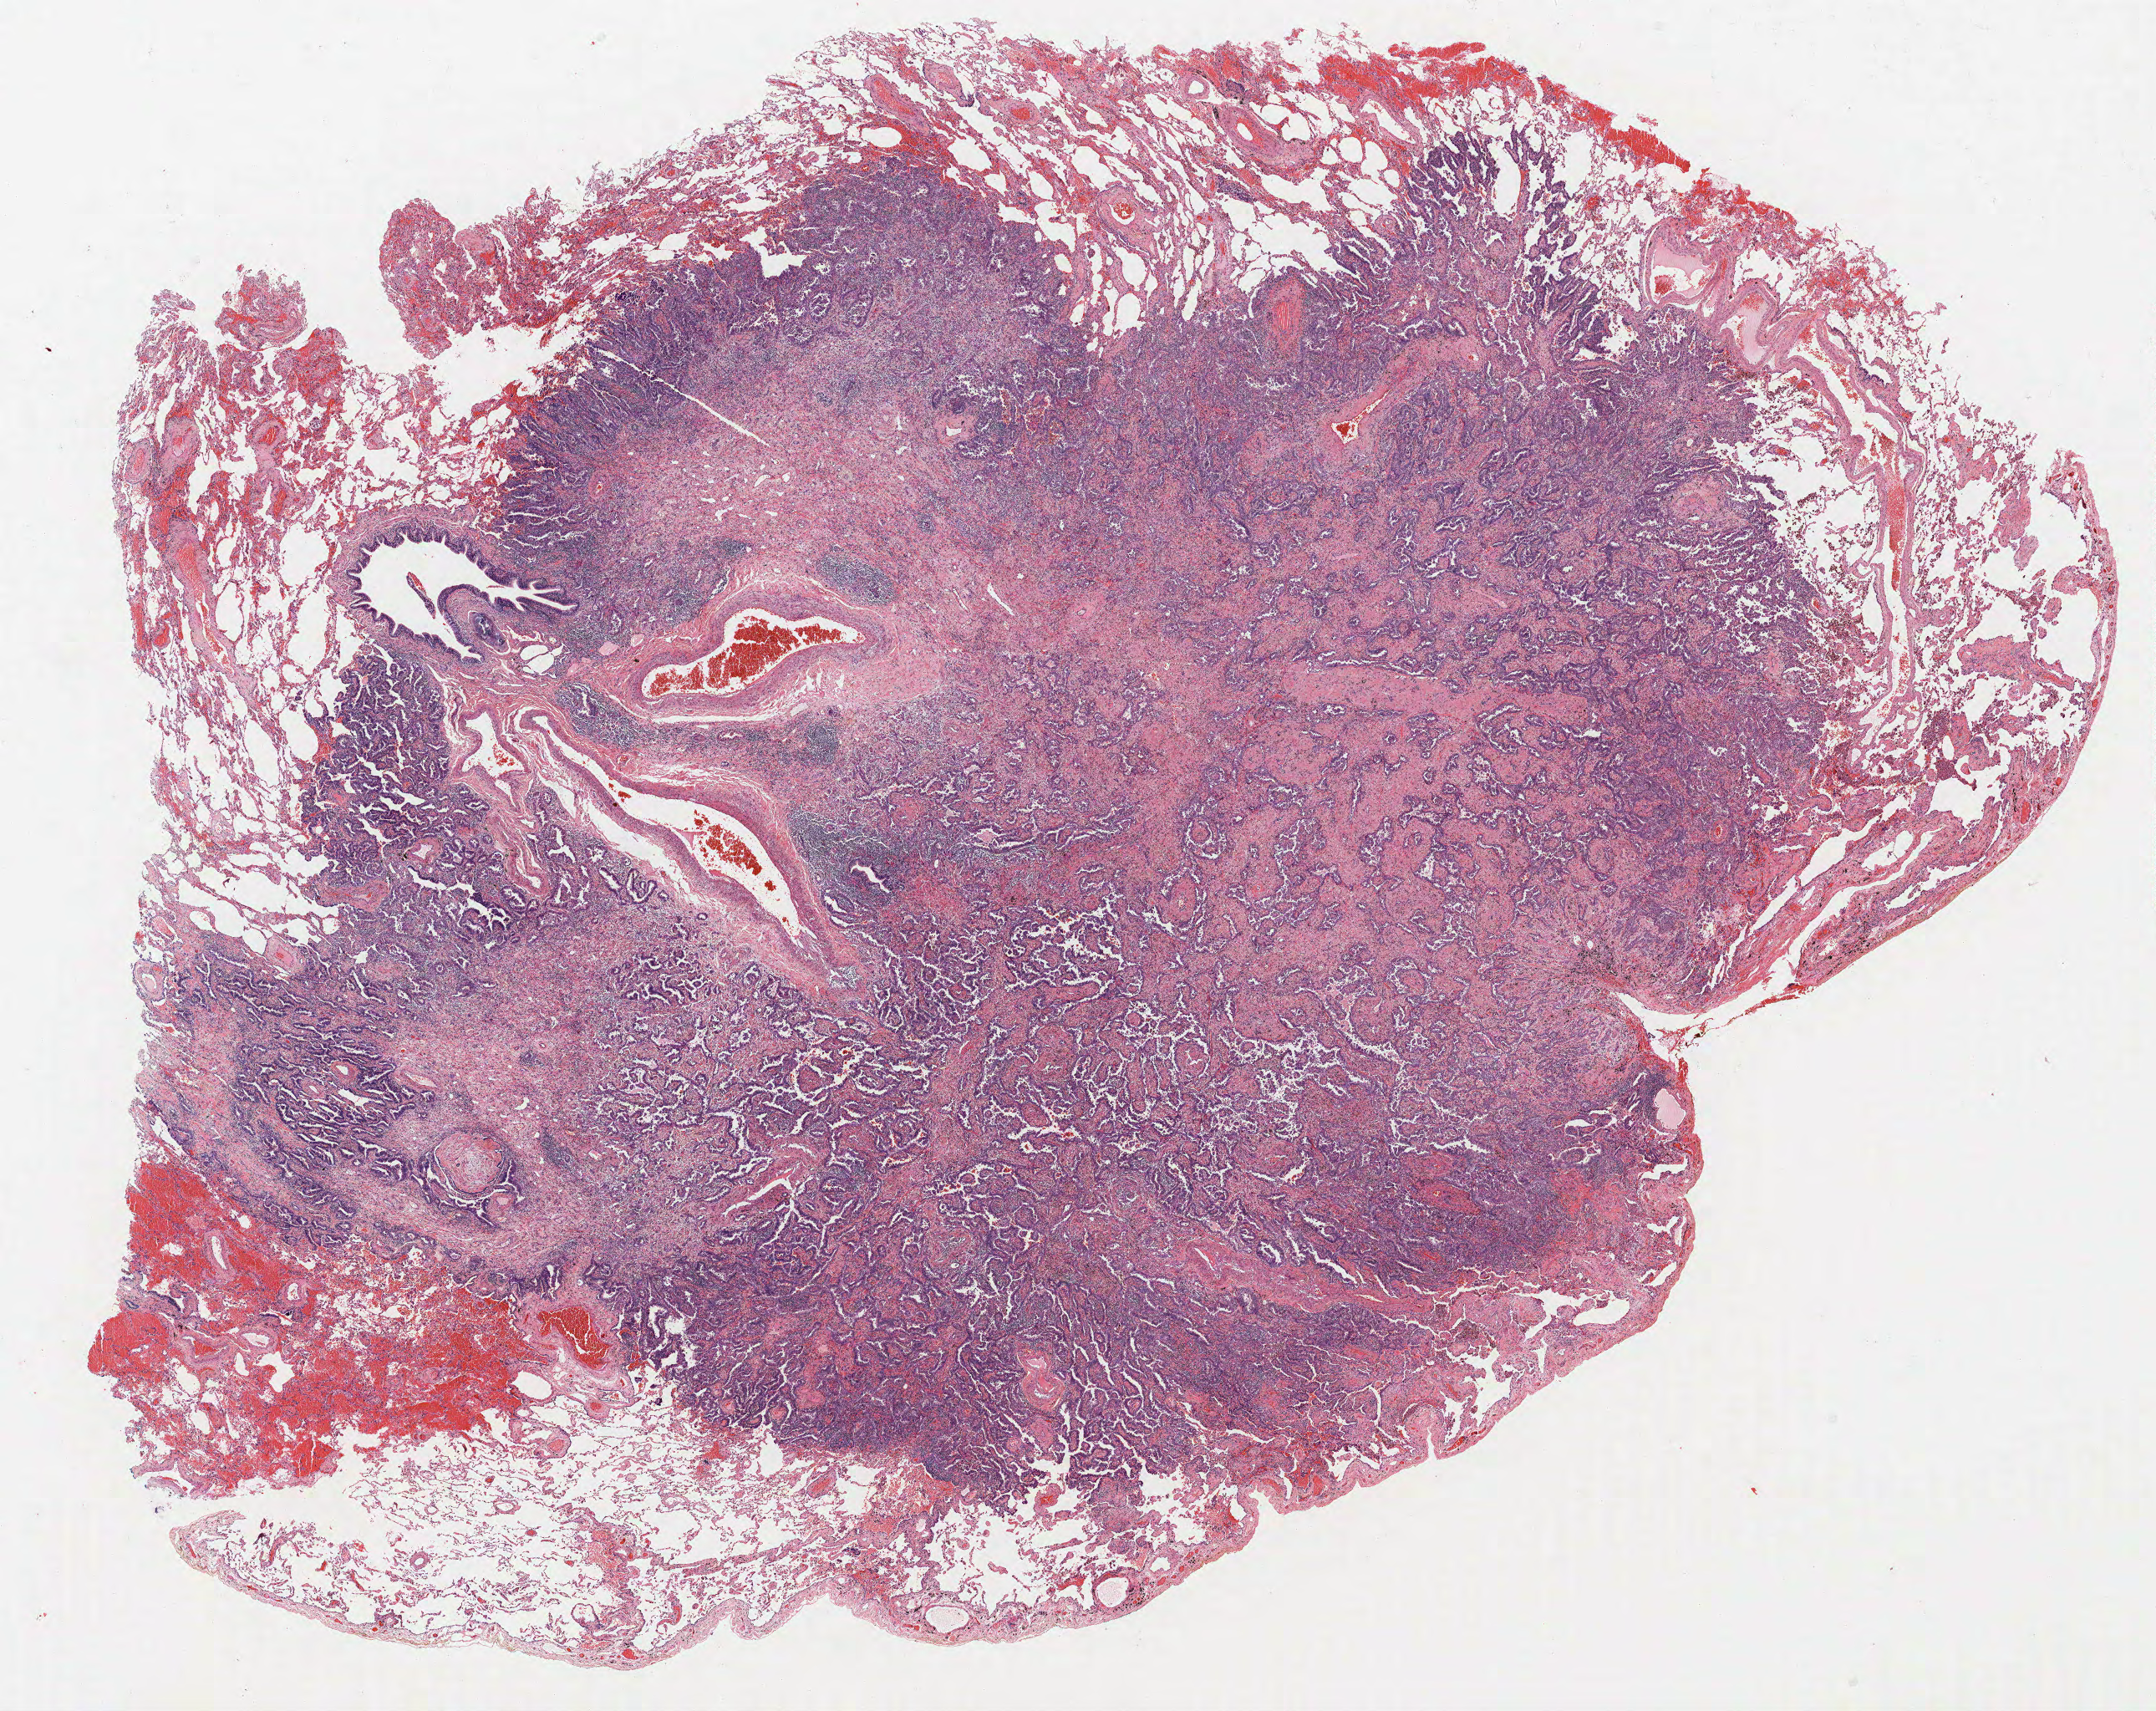
Whole-slide histology image, H&E-stained — a low-resolution overview of the entire scanned area, about 20.6 x 16.4 mm; formalin-fixed paraffin-embedded (FFPE) section; lung. Male, age 74 at enrolment. Current smoker at enrolment. Grade: moderately differentiated (G2).
• tumour size (pathology): 16 mm
• participant's lung-cancer diagnosis: Bronchiolo-alveolar adenocarcinoma, NOS
• ICD-O-3 topography: lower lobe of lung (C34.3)
• stage (AJCC 6th edition): IA
• primary tumour location (clinical record): right lower lobe